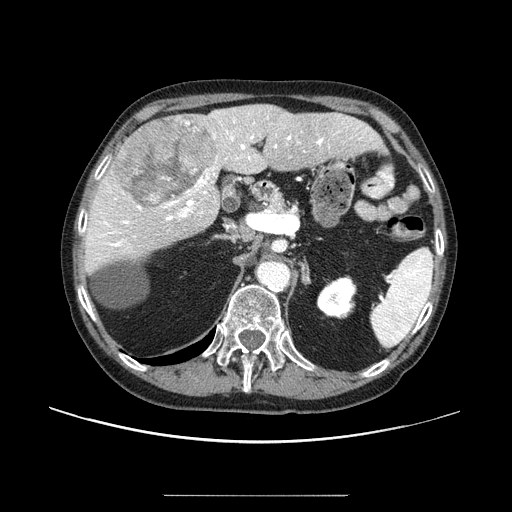
Contrast-enhanced abdominal CT (liver protocol), one axial slice. Slice 53 of 91 in the series (ordered by position). One of 2 acquisitions stored at this slice position. Soft-tissue window (W 400 / L 40 HU). 2.5 mm slice thickness. 512 × 512 image matrix, field of view 400 × 400 mm. Case-level facts recorded for this patient, not image findings: diagnosis: hepatocellular carcinoma (patient treated with transarterial chemoembolisation; whether this scan precedes or follows treatment is not stated here); TNM stage (as recorded): Stage-I; Child-Pugh class: A; tumour nodularity: uninodular.
Structures marked on this image (semi-automatically segmented with operator editing):
- liver parenchyma outside the tumour (the mass and vessels are separate outlines, so this box may not span the whole liver): box from (x=84, y=104) to (x=382, y=274) px
- mass: (x=112, y=114)–(x=218, y=208)
- liver vessels: (x=89, y=116)–(x=371, y=247)